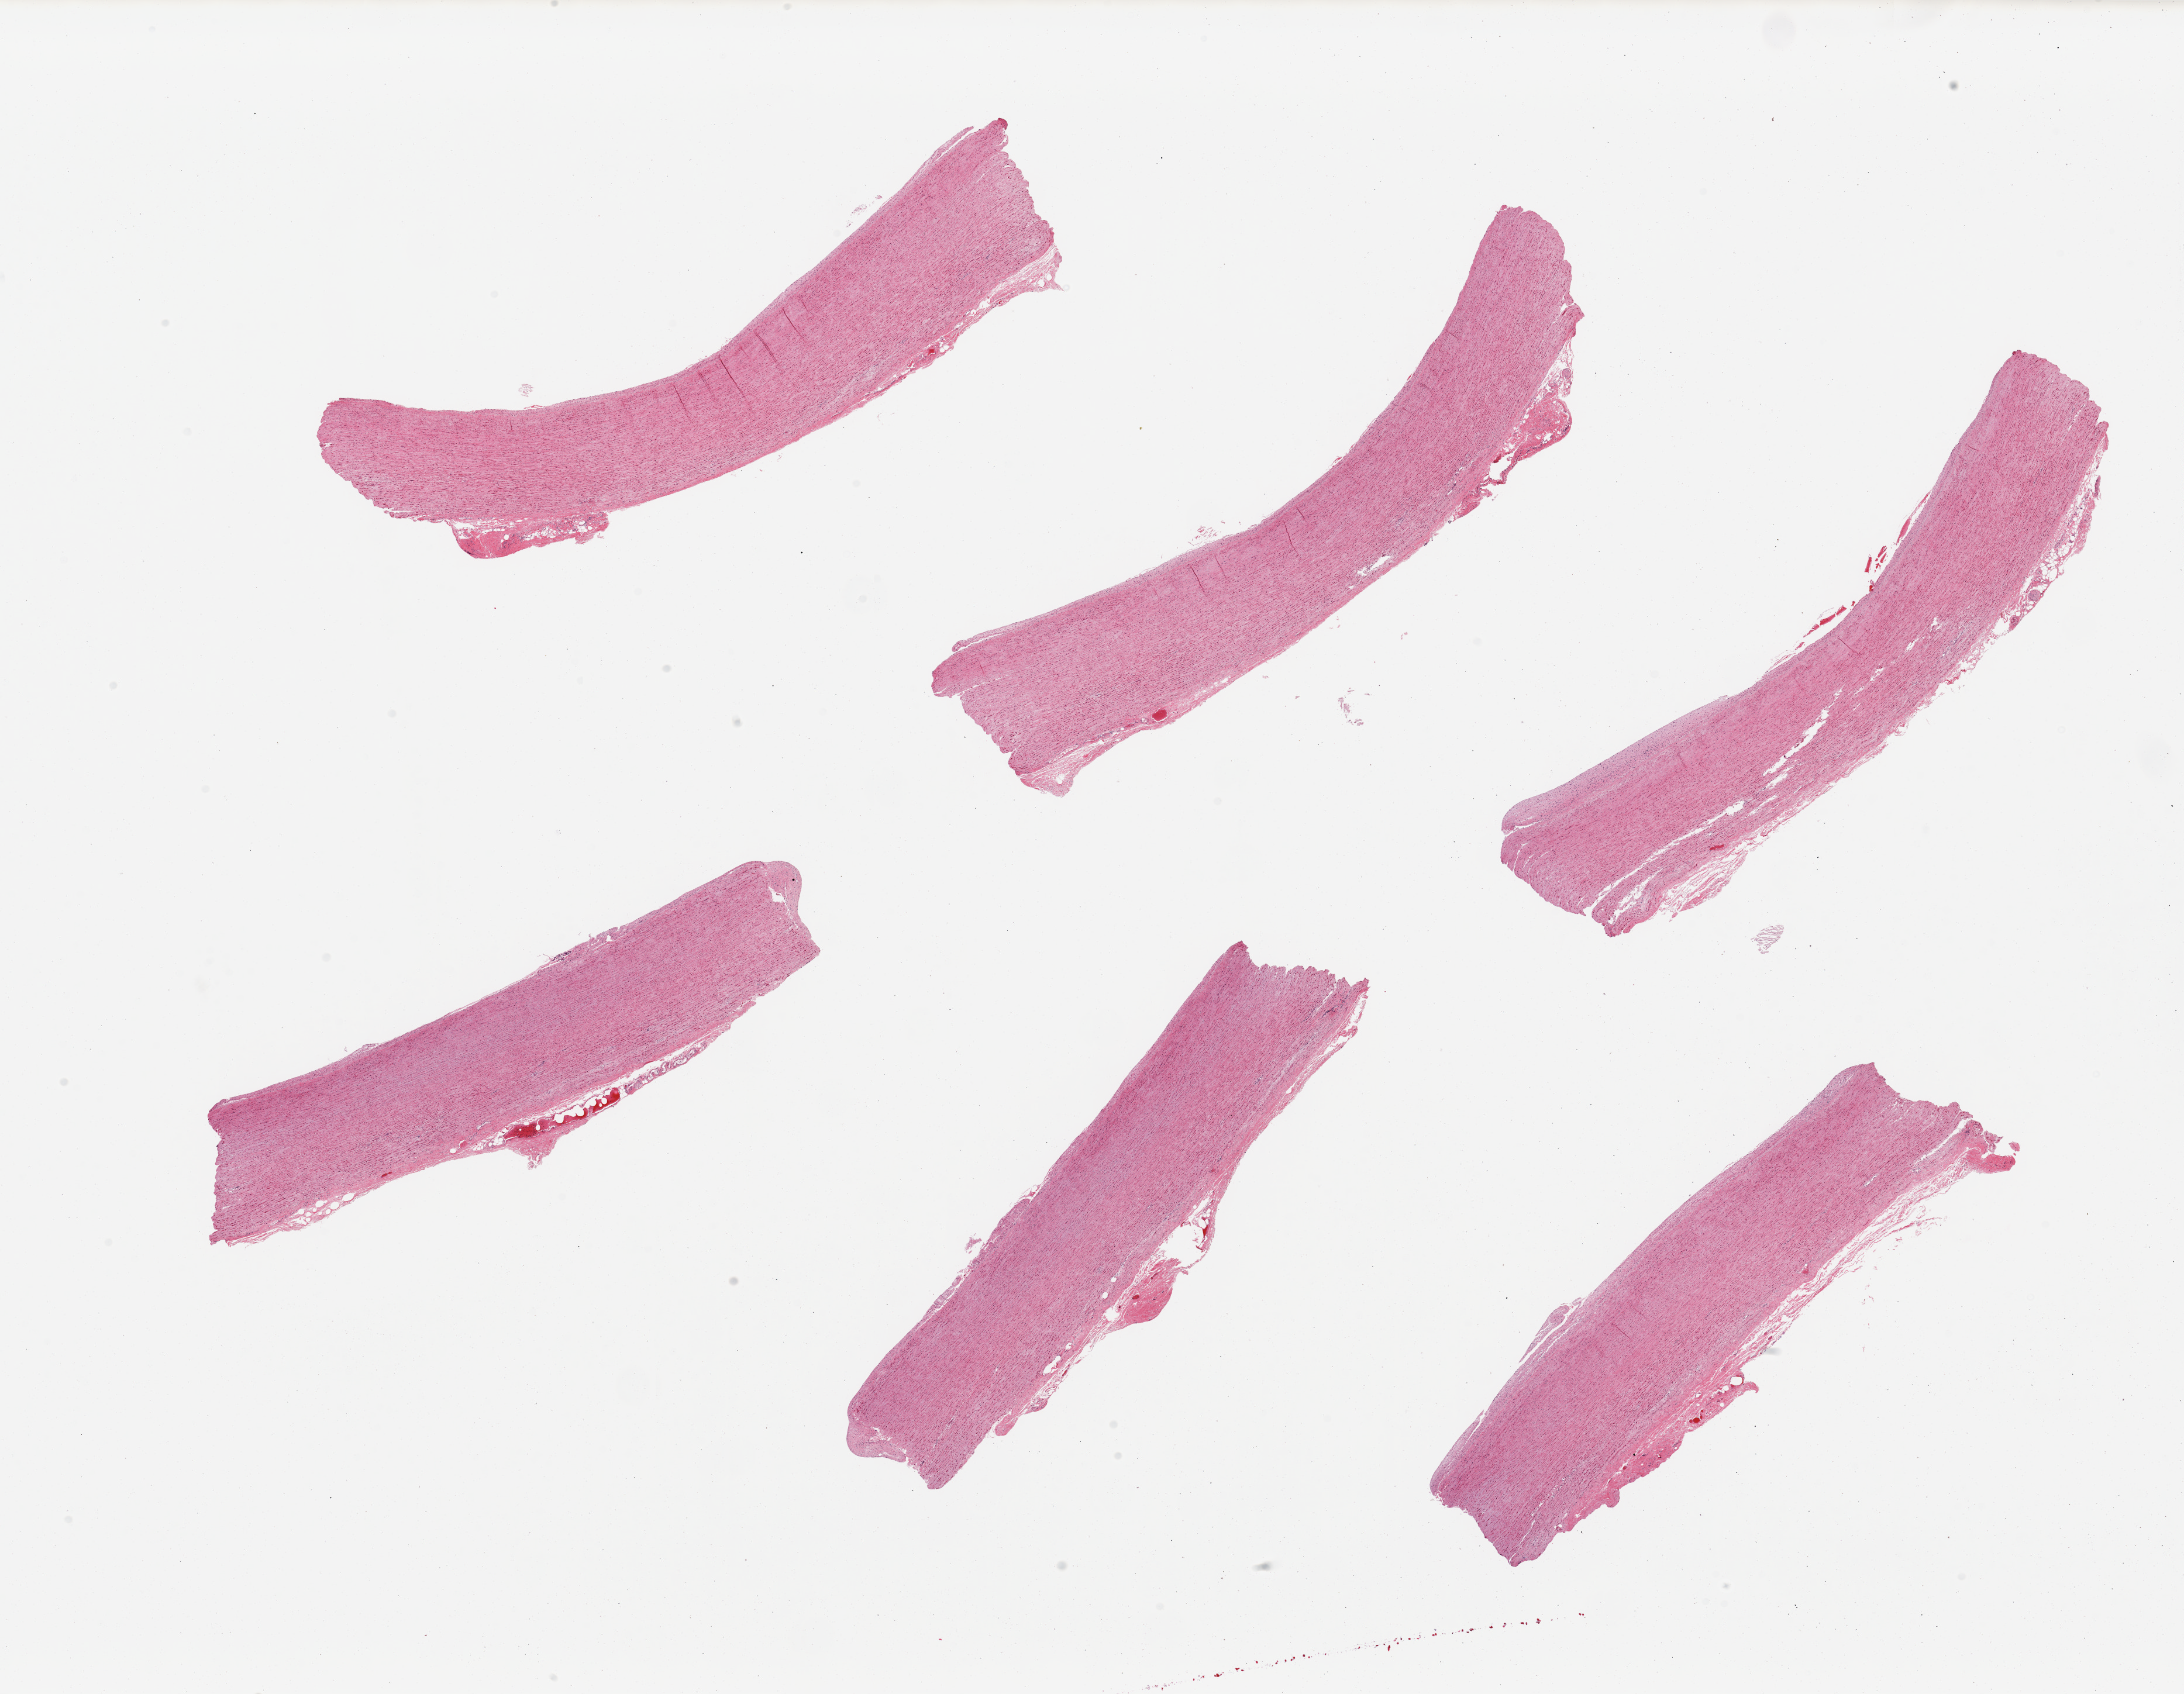
Whole-slide image, haematoxylin and eosin stain, brightfield — low-resolution overview of the scanned area, about 29.5 x 22.9 mm (slide scanned at 20x). PAXgene-fixed, paraffin-embedded tissue. Sampled site (target tissue): aorta. Donor tissue sample.
Review note (as recorded): 6 pieces; well trimmed; no plaques.